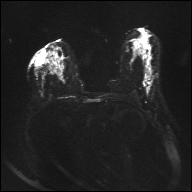
Breast MRI, one axial slice; diffusion-weighted series; image 2 of 4 stored at this slice position (different b-values; order by instance number); 1.5 T; 4 mm slice thickness; 192 × 192 image matrix, field of view 360 × 360 mm. Female patient.
Outlined on this slice (manually delineated by an expert):
- tumour on diffusion-weighted imaging: bounding box [x1, y1, x2, y2] px = [145, 77, 152, 85]